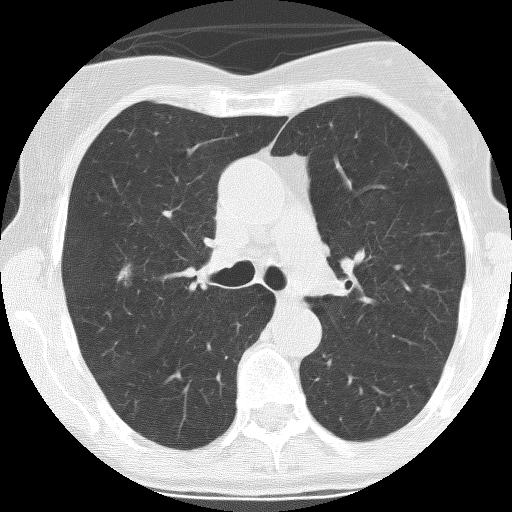
Low-dose screening chest CT, one axial slice. Slice 171 of 261 in the series (ordered by position). Reconstruction kernel BONE. 120 kVp. Lung window (W 1500 / L -600 HU). 2.5 mm slice thickness. 512 × 512 image matrix, field of view 270 × 270 mm.
Annotated regions visible in this slice (expert manual segmentation):
- lesion 1 (tumor, upper lobe of right lung): bounding box [x1, y1, x2, y2] px = [117, 265, 134, 285]